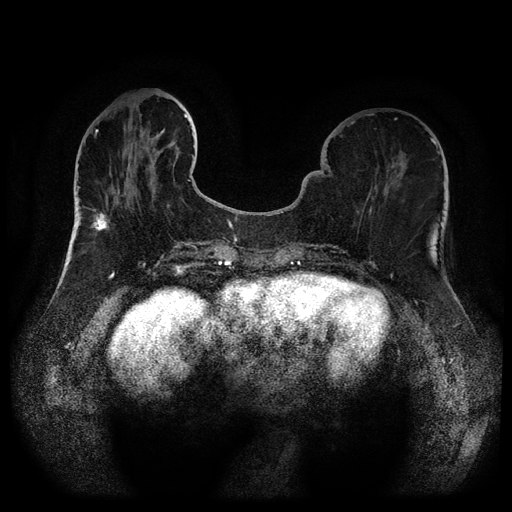
Breast MRI (dynamic contrast-enhanced, multi-phase), one axial slice. Position 33 of 116 along the scan axis. Dynamic contrast-enhanced series, time point 2 of 5 at this slice position (early post-contrast). 1.5 T. TE 2.6 ms, TR 5.3 ms. 512 × 512 image matrix, field of view 350 × 350 mm. Patient: female, 75 years.
Annotated regions visible in this slice (semi-automatic segmentation, software-assisted and operator-edited):
- breast lesion (labelled benign in the annotation): bounding box <90,210,113,234> (left, top, right, bottom; pixels)